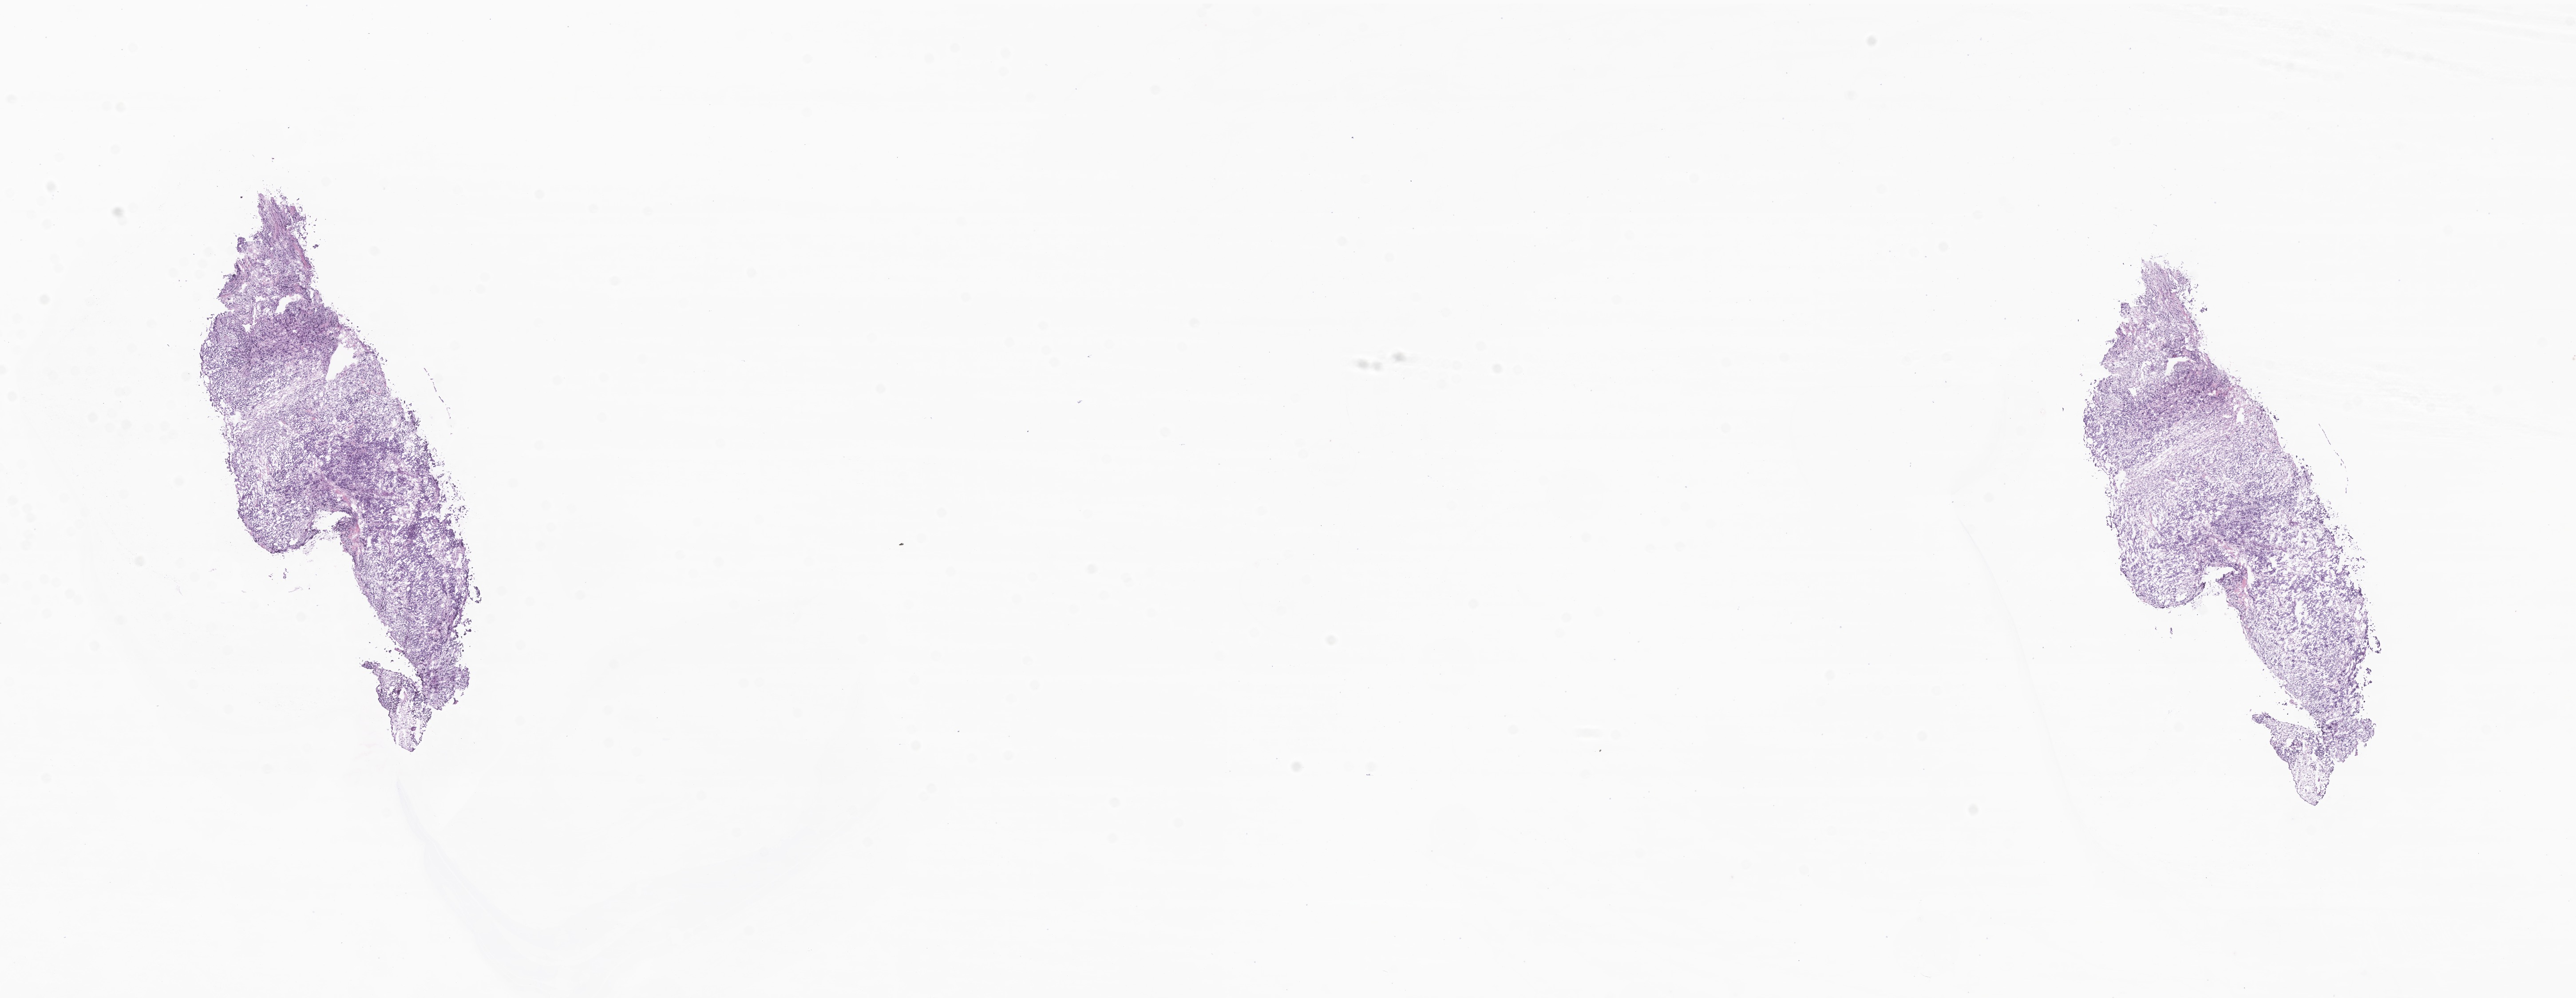
Digitized hematoxylin and eosin (H&E)-stained section of tumor tissue from the soft tissue of upper extremity, a low-resolution overview of the entire scanned area, about 24.5 x 9.5 mm, cryosection (OCT / tissue freezing medium). Female patient, age 169 months (14 years 1 month).
- diagnosis (ICD-O-3 morphology term): Alveolar rhabdomyosarcoma